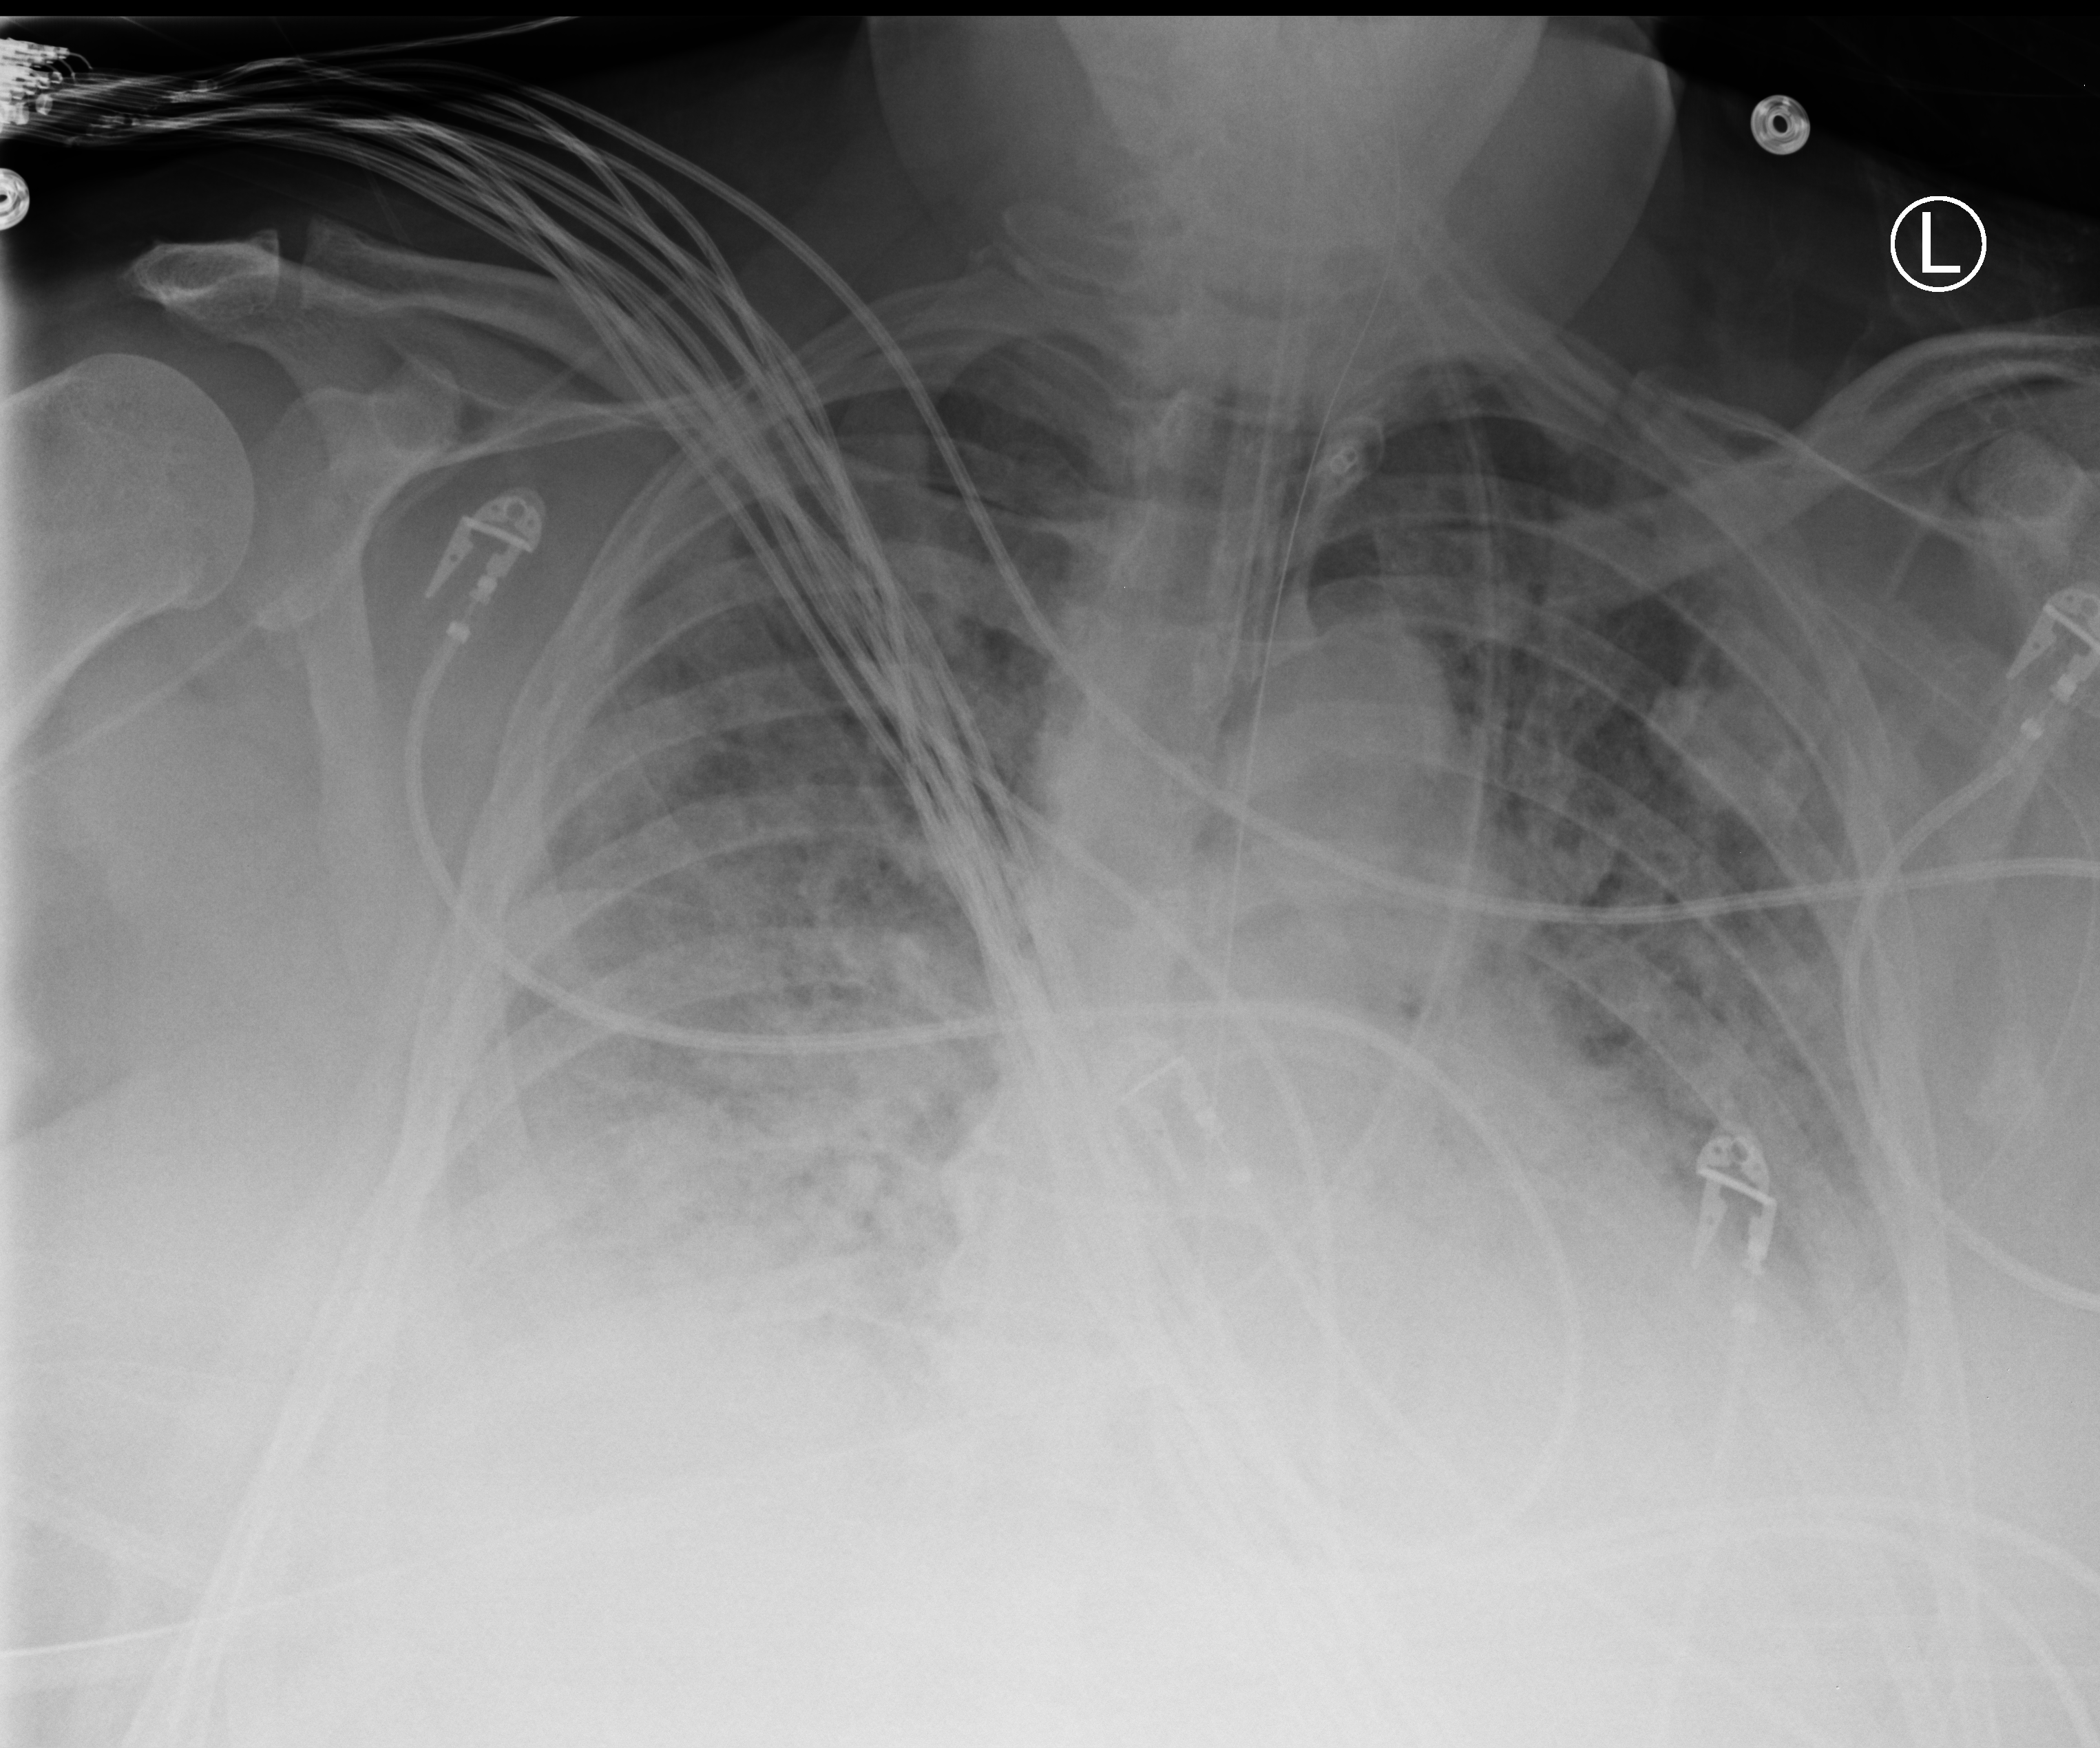
Chest X-ray (portable). Patient hospitalised with COVID-19; male, aged 60–74 years.
Admission-level facts for this patient (not findings on this image; timing relative to this image not recorded): chronic kidney disease (admission record): no; mechanically ventilated during this hospital stay: yes.